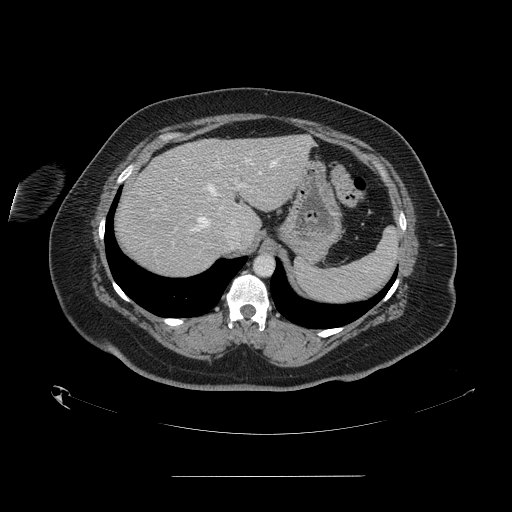
Contrast-enhanced abdominal CT, one axial slice; position 116 of 164 along the scan axis; 120 kVp; soft-tissue window (W 400 / L 40 HU); 2.5 mm slice thickness; 512 × 512 image matrix, field of view 495 × 495 mm. Female patient, age 52 years. From the clinical record (not read from this slice): diagnosis: colorectal cancer liver metastases, imaged before liver resection; multiple liver metastases: yes; largest metastasis: 3.5 cm; disease in both lobes: no.
Outlined on this slice (expert manual segmentation):
- hepatic veins: bounding box <172,158,276,244> (left, top, right, bottom; pixels)
- liver: <115,136,312,278>
- planned liver remnant (the part of the liver to remain after resection): <170,136,312,226>
- portal vein (with intrahepatic branches): <175,178,244,209>